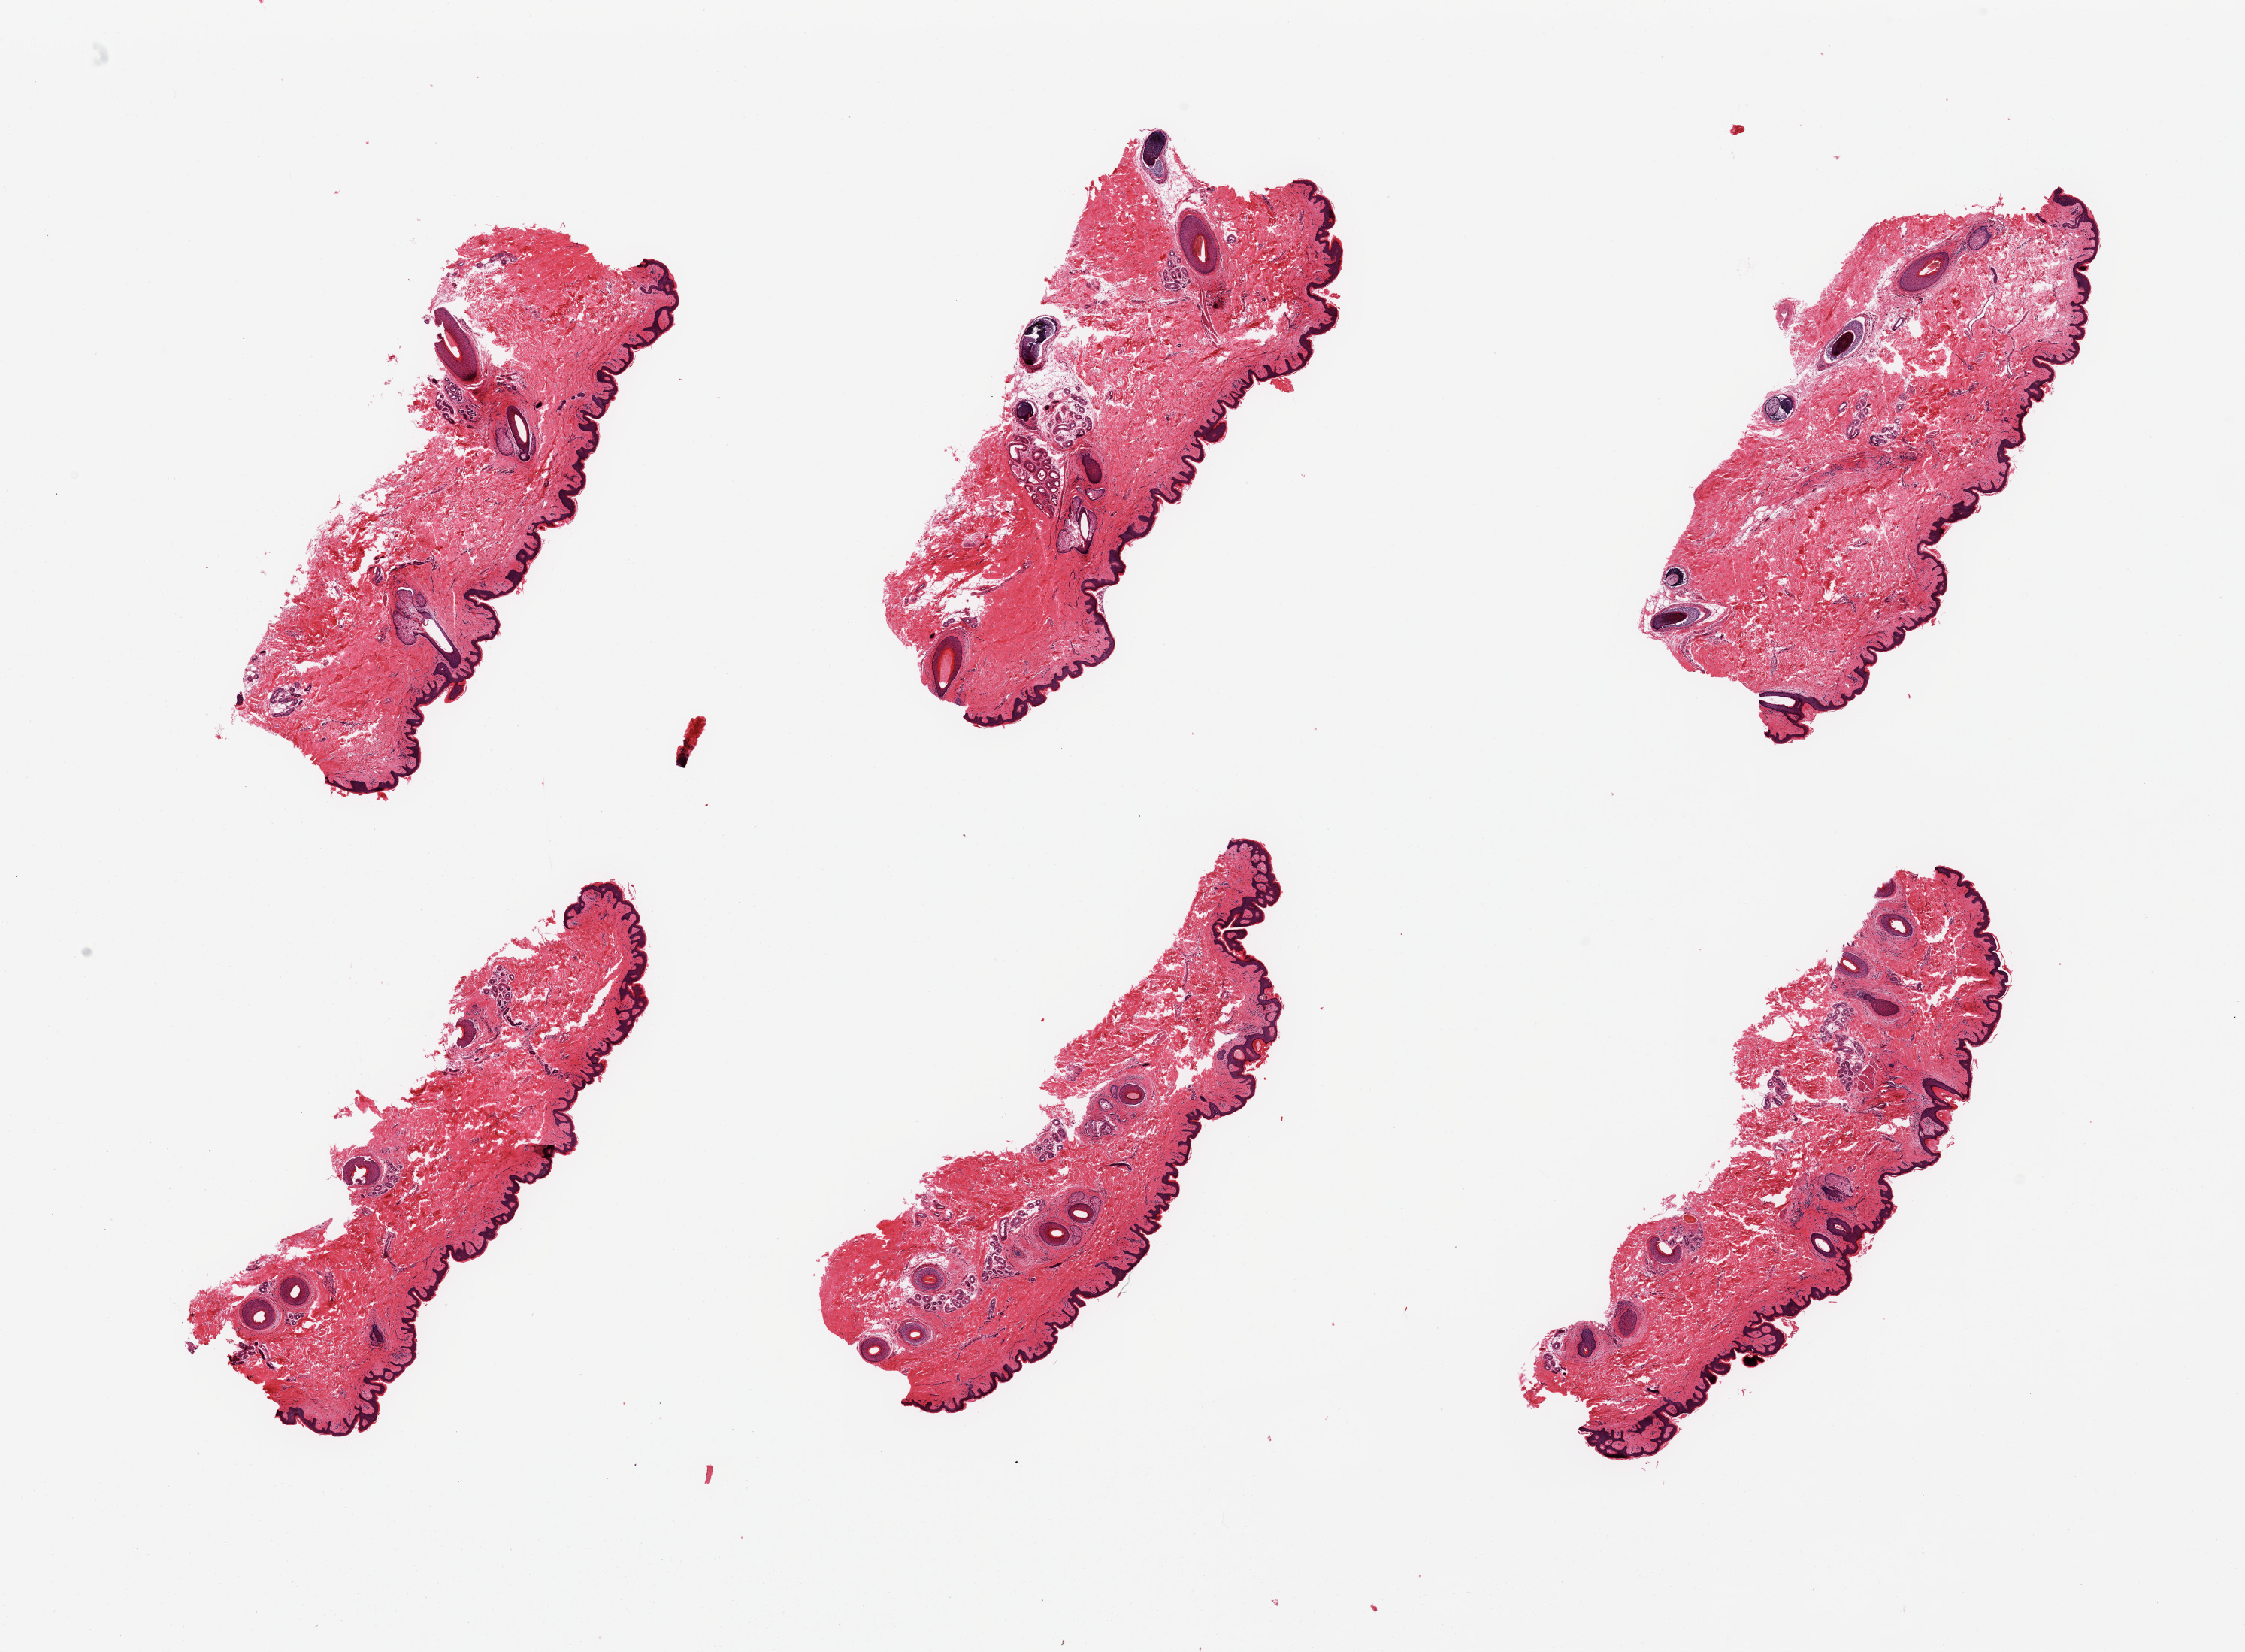
H&E whole-slide image — shown as a low-resolution overview of the whole scanned area (about 23.6 x 17.4 mm). PAXgene-fixed paraffin-embedded (PFPE) section. Target tissue: skin of suprapubic region. Donor tissue sample. Donor: male.
Reviewer comment on this tissue sample: 6 pieces, no significant adherent dermal fat; squamous epithelium is ~50-60 microns.